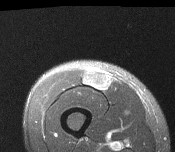
MRI of an extremity soft-tissue mass, one axial slice; position 40 of 116 along the scan axis; T2-weighted fat-saturated; MR volume resampled by the dataset authors to the PET/CT grid (not the native acquisition matrix); 3.27 mm slice thickness; 175 × 152 image matrix, field of view 171 × 148 mm. Male patient. From the clinical record (not read from this slice): histological type: pleiomorphic leiomyosarcoma; grade: intermediate; site of the primary tumour: right thigh.
Outlined on this slice (expert contour drawn on MRI and transferred to this co-registered scan by the dataset authors):
- gross tumour volume including surrounding oedema: box from (x=83, y=72) to (x=110, y=89) px